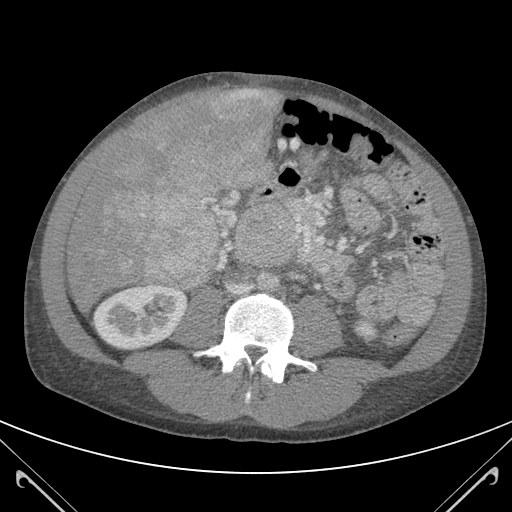
Contrast-enhanced abdominal CT (liver protocol), one axial slice. Slice 40 of 118 in the series (ordered by position). 120 kVp. Soft-tissue window (W 400 / L 40 HU). 512 × 512 image matrix. From the clinical record (not read from this slice): diagnosis: hepatocellular carcinoma (patient treated with transarterial chemoembolisation; whether this scan precedes or follows treatment is not stated here); TNM stage (as recorded): Stage-IIIB; Child-Pugh class: A.
Annotated regions visible in this slice (semi-automatic segmentation, software-assisted and operator-edited):
- liver parenchyma outside the tumour (the mass and vessels are separate outlines, so this box may not span the whole liver): bounding box [x1, y1, x2, y2] px = [67, 89, 280, 310]
- mass: [91, 90, 275, 281]
- liver vessels: [198, 266, 207, 280]